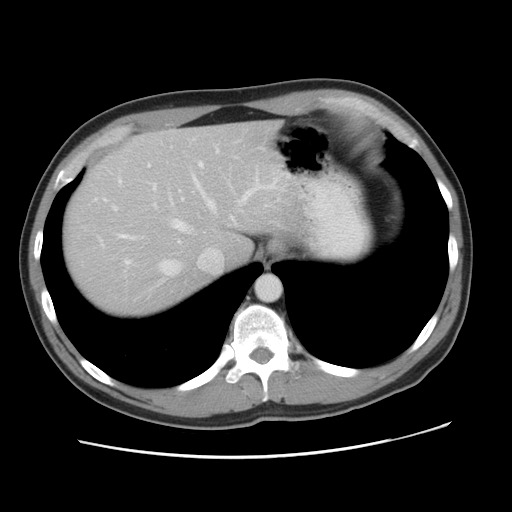
Contrast-enhanced abdominal CT, one axial slice; slice 39 of 49 in the series (ordered by position); reconstruction kernel STANDARD; 120 kVp; intravenous contrast given; soft-tissue window (W 400 / L 40 HU); 5 mm slice thickness; 512 × 512 image matrix, field of view 363 × 363 mm. Male patient, age 41 years. Case-level facts recorded for this patient, not image findings: diagnosis: colorectal cancer liver metastases, imaged before liver resection; multiple liver metastases: yes; largest metastasis: 0.7 cm.
Structures marked on this image (manually delineated by an expert):
- hepatic veins: bounding box [x1, y1, x2, y2] px = [103, 173, 275, 276]
- liver: [63, 122, 289, 318]
- planned liver remnant (the part of the liver to remain after resection): [104, 122, 289, 267]
- portal vein (with intrahepatic branches): [95, 150, 276, 263]